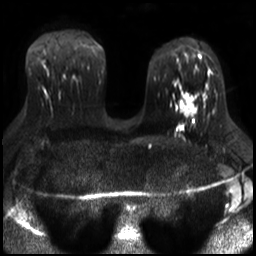
Breast MRI, one axial slice; position 17 of 30 along the scan axis; diffusion-weighted series; image 2 of 4 stored at this slice position (different b-values; order by instance number); 3 T; 4 mm slice thickness; 256 × 256 image matrix, field of view 320 × 320 mm. Female patient.
Annotated regions visible in this slice (expert manual segmentation):
- tumour on diffusion-weighted imaging: bounding box <180,100,195,115> (left, top, right, bottom; pixels)